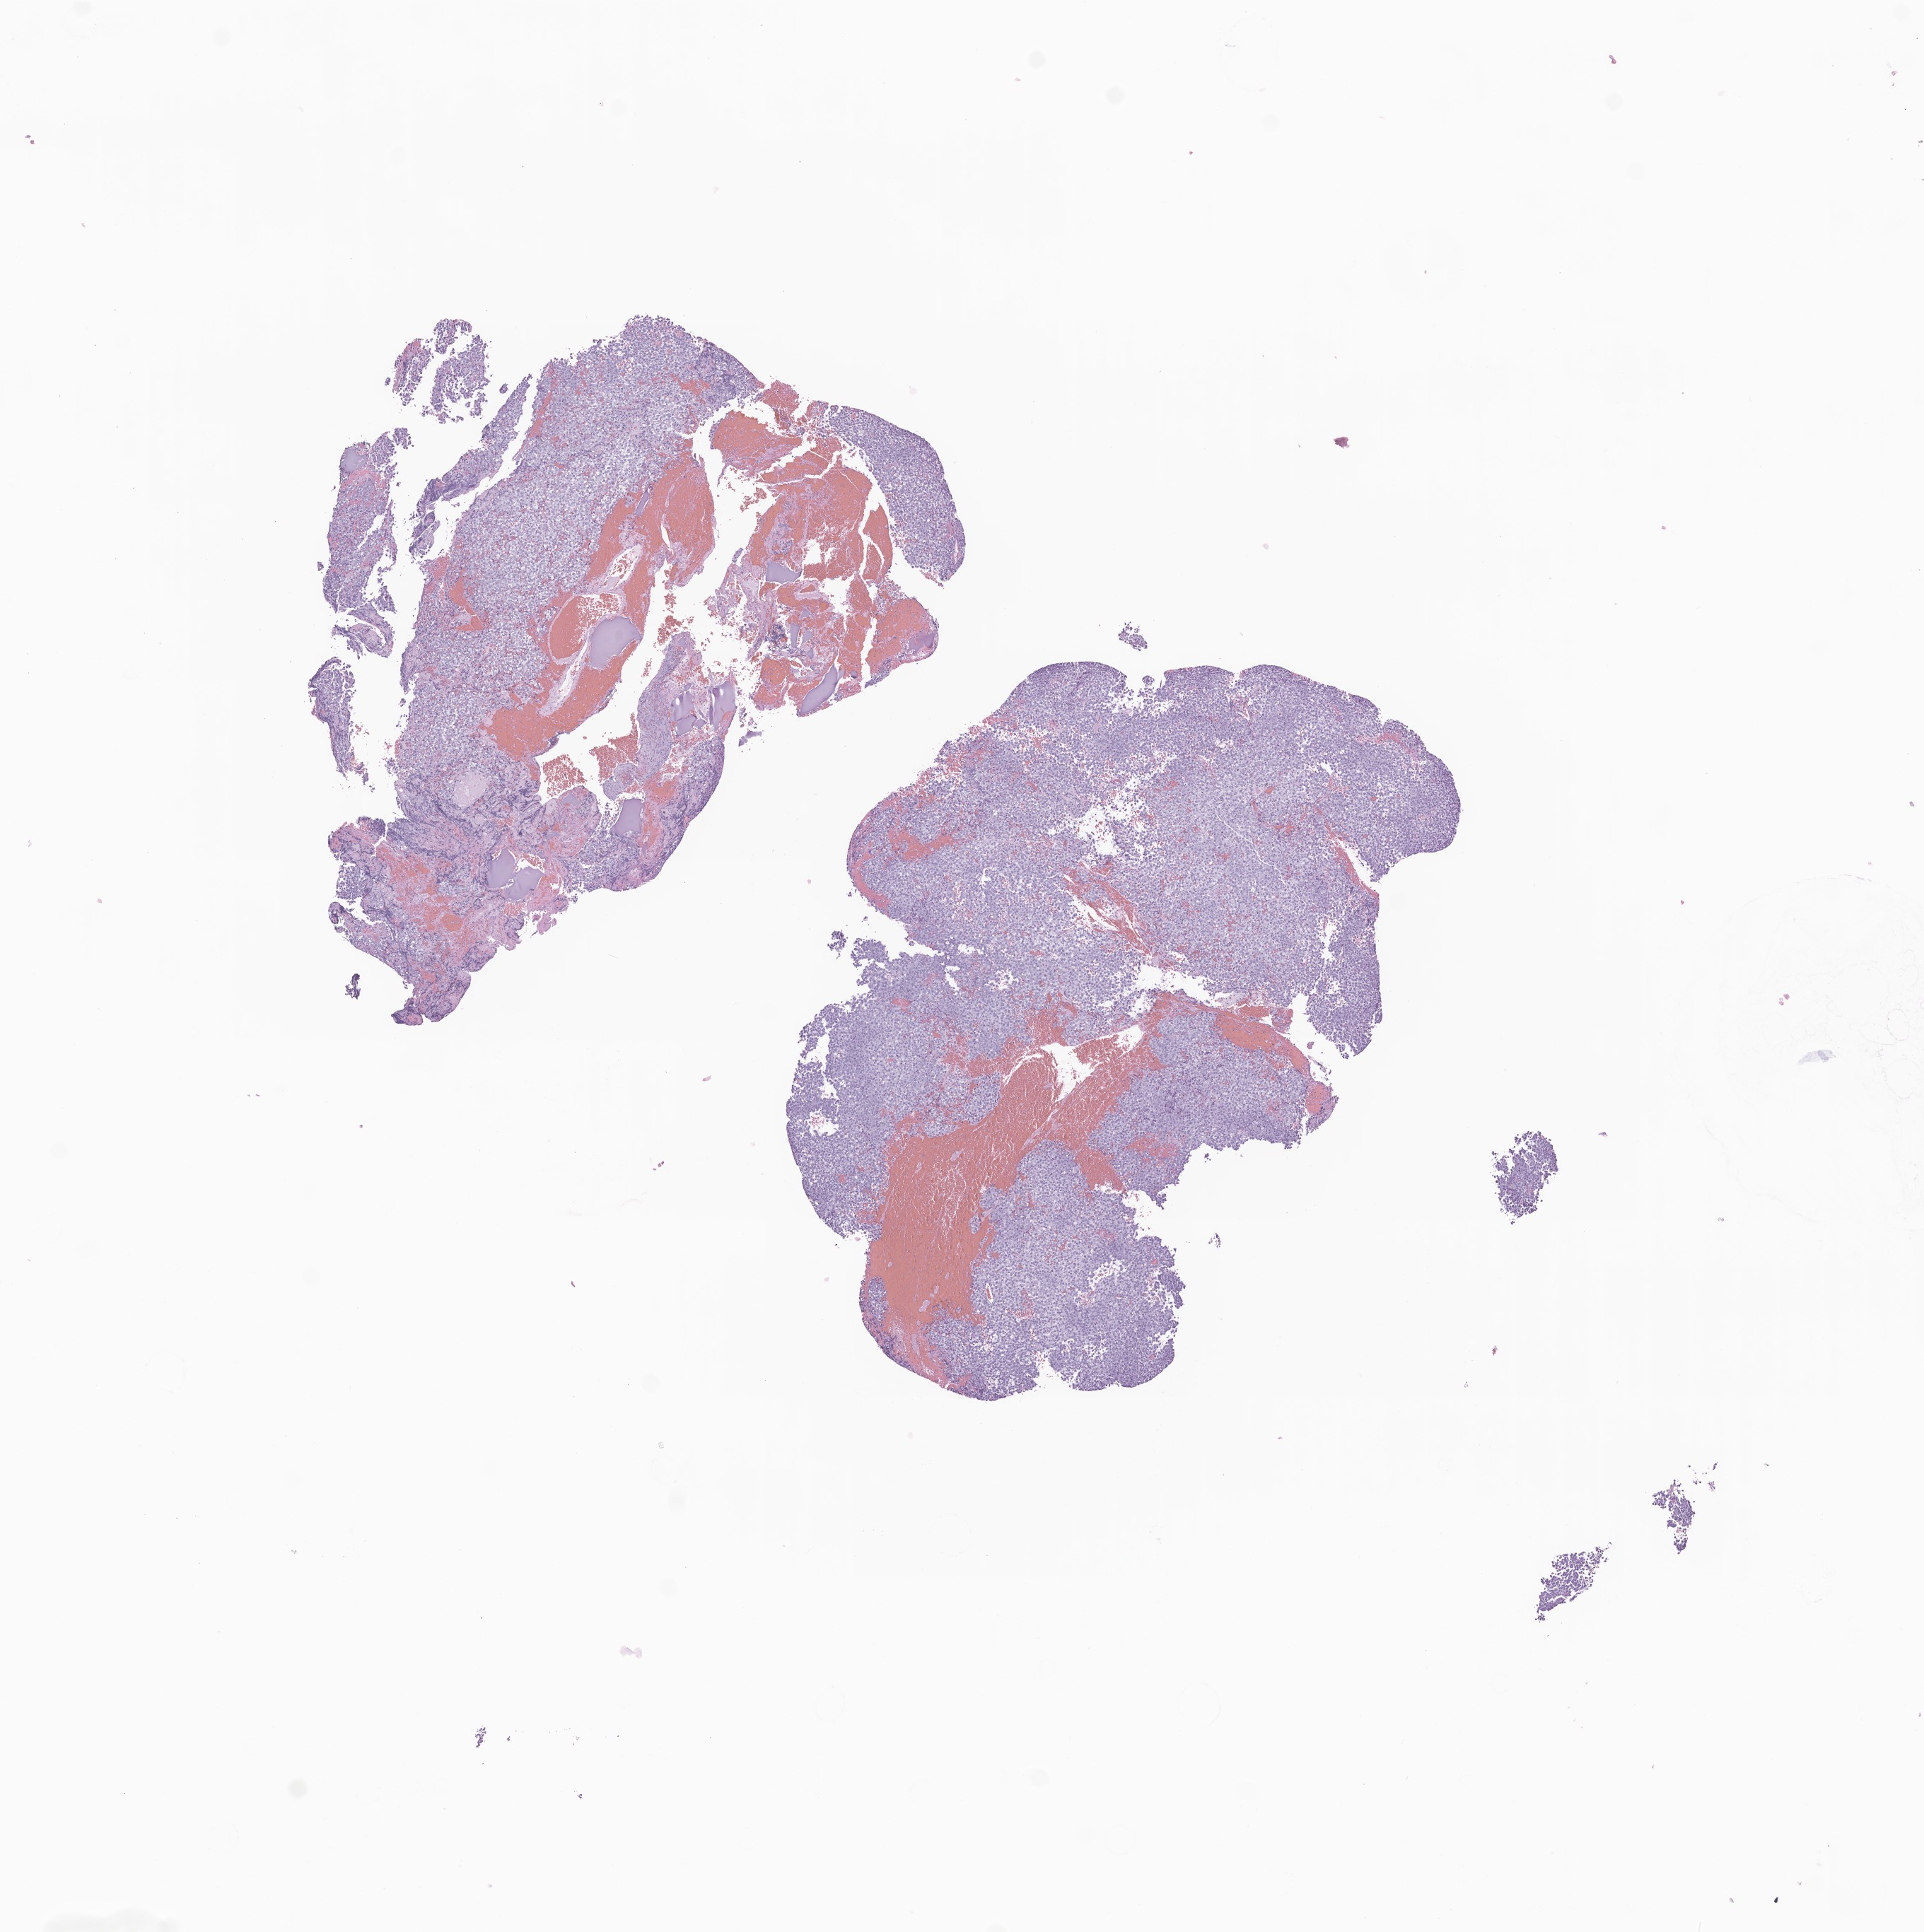
Whole-slide image, haematoxylin and eosin stain of tumor tissue from the pineal gland, a low-resolution overview of the entire scanned area, about 11.5 x 11.5 mm, FFPE section. Patient: male, age 177 months (14 years 9 months).
Recorded diagnosis: Germinoma.